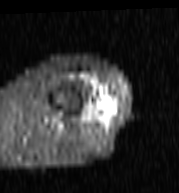
MRI of an extremity soft-tissue mass, one axial slice. Slice 25 of 103 in the series (ordered by position). STIR. MR volume resampled by the dataset authors to the PET/CT grid (not the native acquisition matrix). 3.27 mm slice thickness. 179 × 193 image matrix, field of view 175 × 188 mm. Female patient. Case-level facts recorded for this patient, not image findings: histological type: undifferentiated – high grade; grade: high; site of the primary tumour: left thigh.
Structures marked on this image (expert contour drawn on MRI and transferred to this co-registered scan by the dataset authors):
- gross tumour volume including surrounding oedema: box from (x=95, y=99) to (x=106, y=109) px